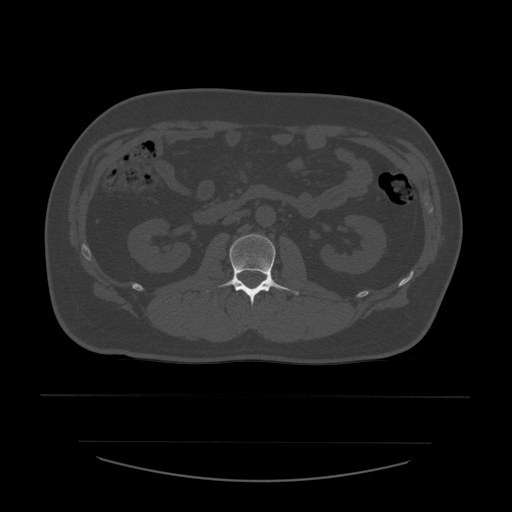
CT including the spine, one axial slice. Position 200 of 532 along the scan axis. 120 kVp. Bone window (W 1800 / L 400 HU). 1.25 mm slice thickness. 512 × 512 image matrix, field of view 441 × 441 mm. Patient age 44 years. Case-level facts recorded for this patient, not image findings: primary cancer: soft tissue sarcoma.
Annotated regions visible in this slice (semi-automatically segmented with operator editing):
- L2 vertebra: bounding box [x1, y1, x2, y2] px = [206, 234, 299, 305]